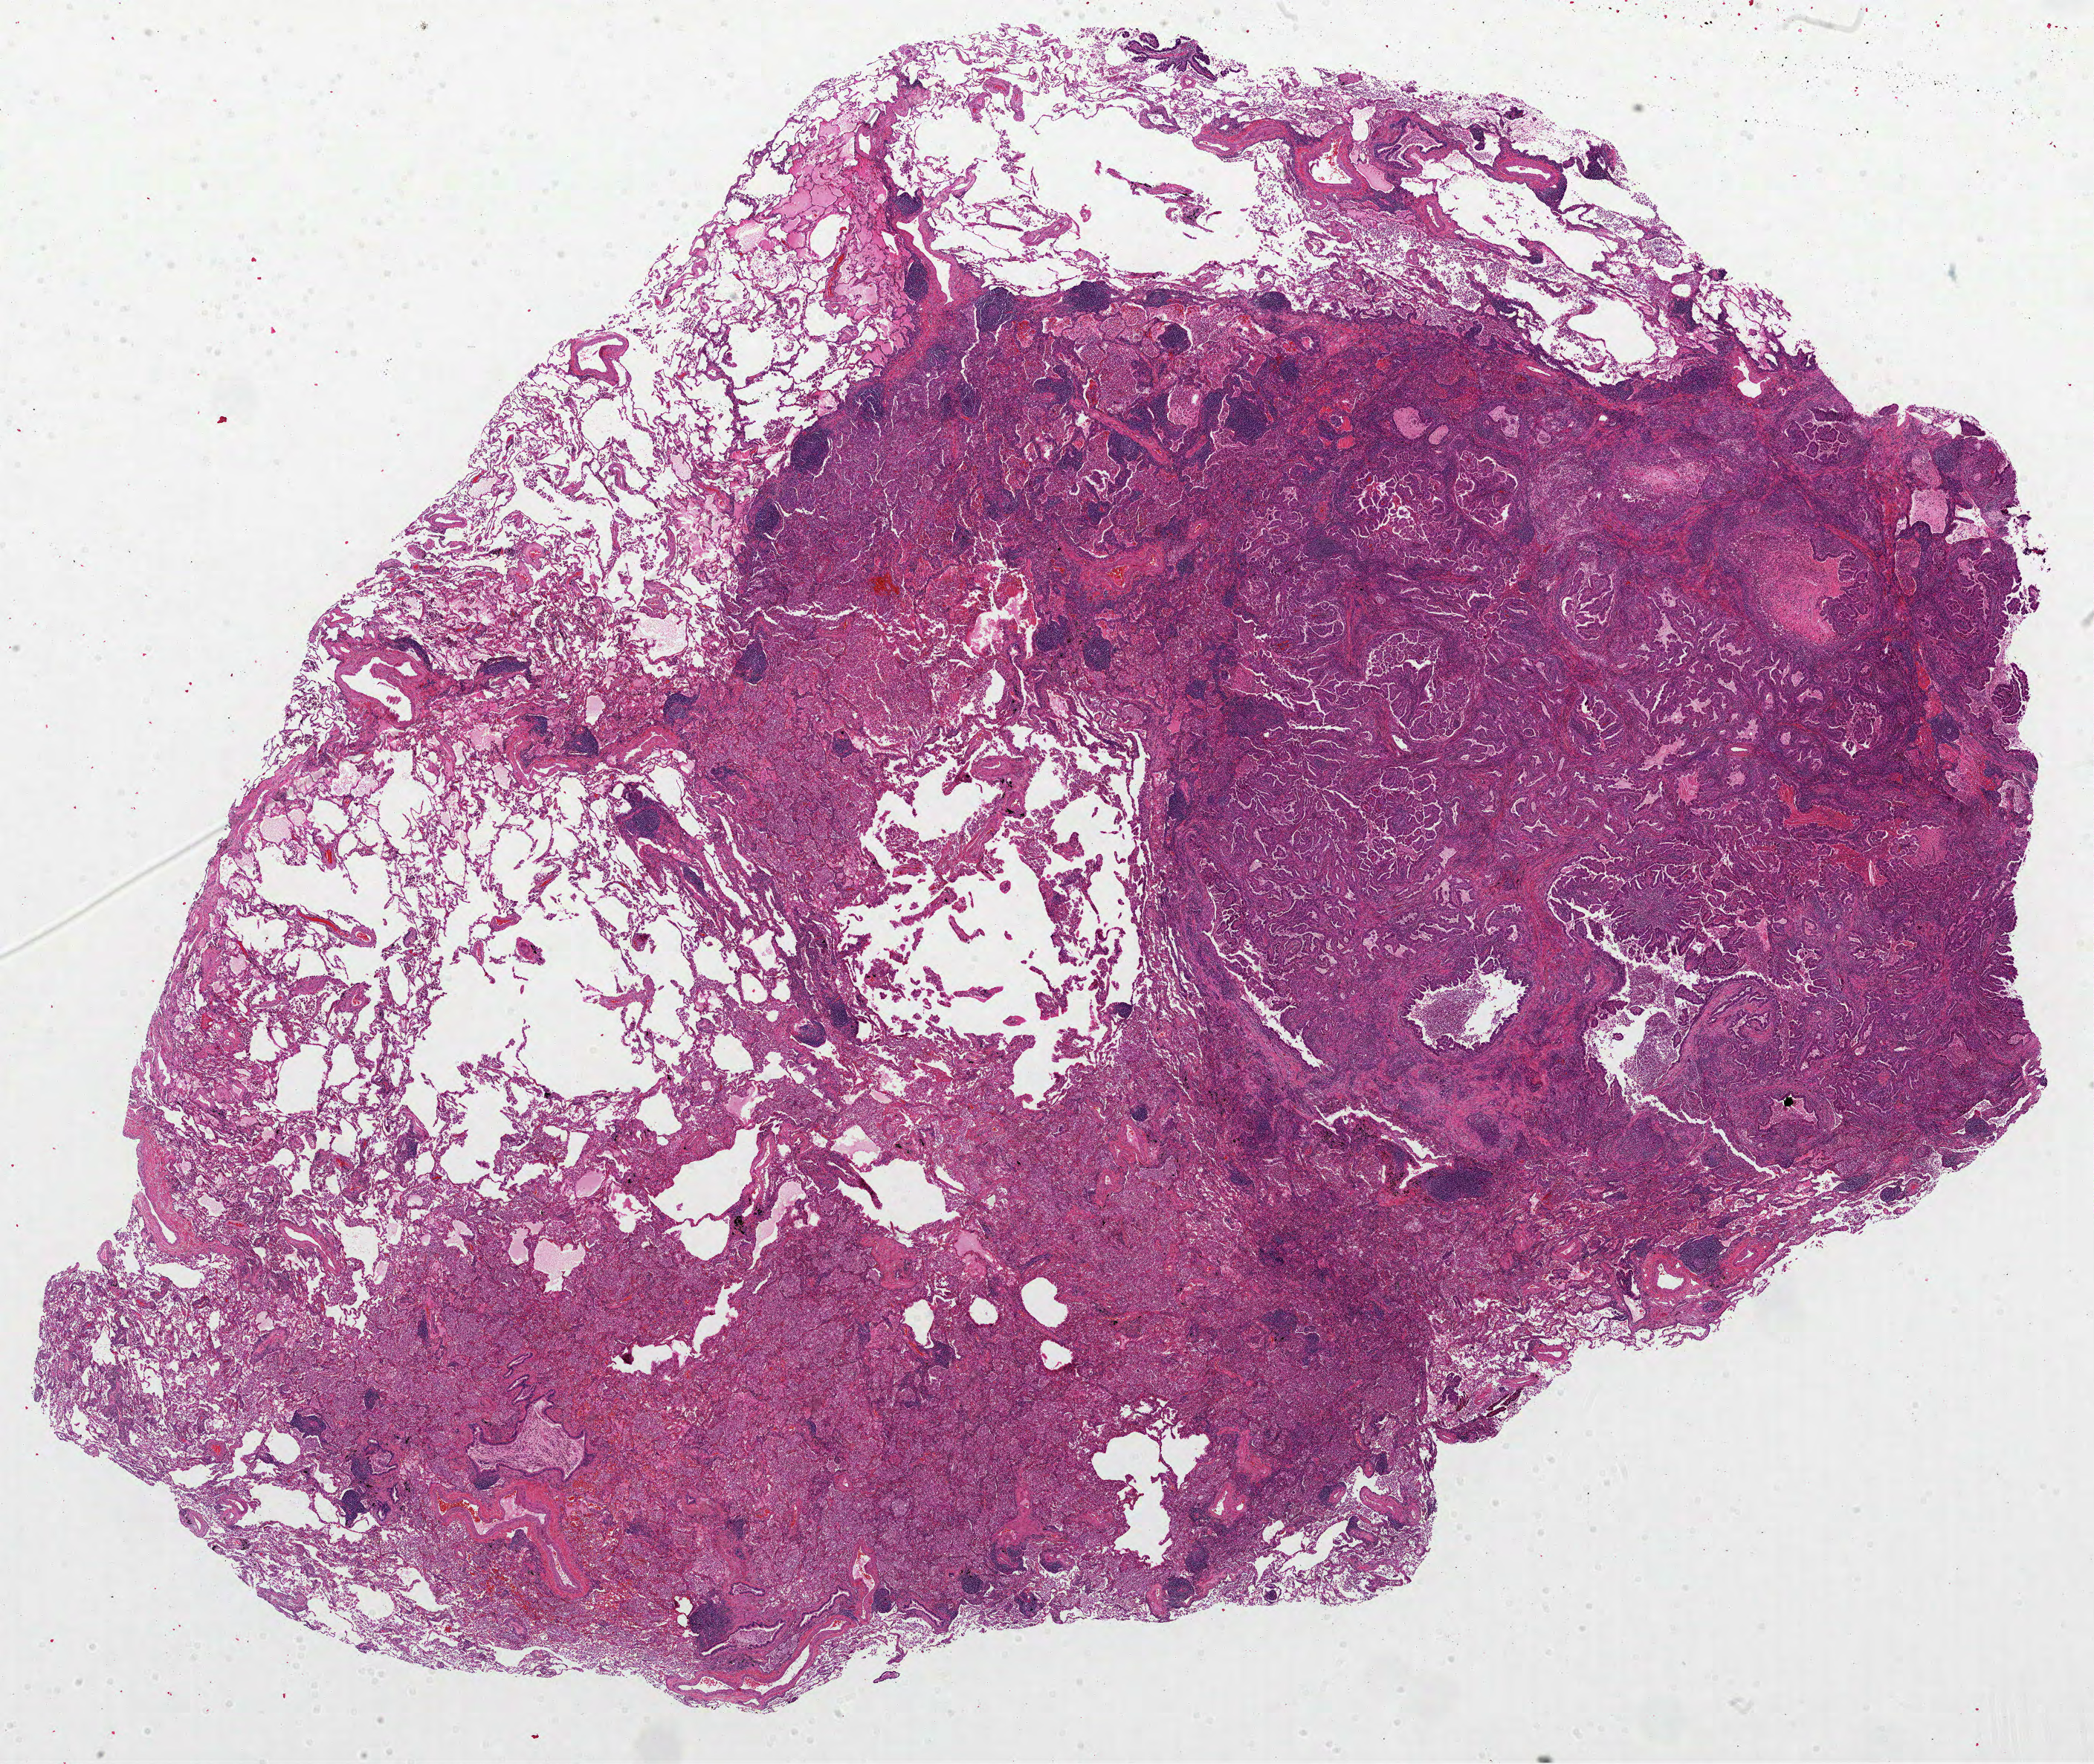
Whole-slide histology image, H&E-stained, shown as a low-resolution overview of the whole scanned area (about 22.7 x 19.1 mm, acquisition: 40x scan), formalin-fixed paraffin-embedded (FFPE) diagnostic section, primary tumour sample from the lung. Female, age 79 years at initial diagnosis.
AJCC pathologic stage: IA (6th edition). Histologic diagnosis: Papillary adenocarcinoma, NOS (upper lobe, lung). Laterality: left.